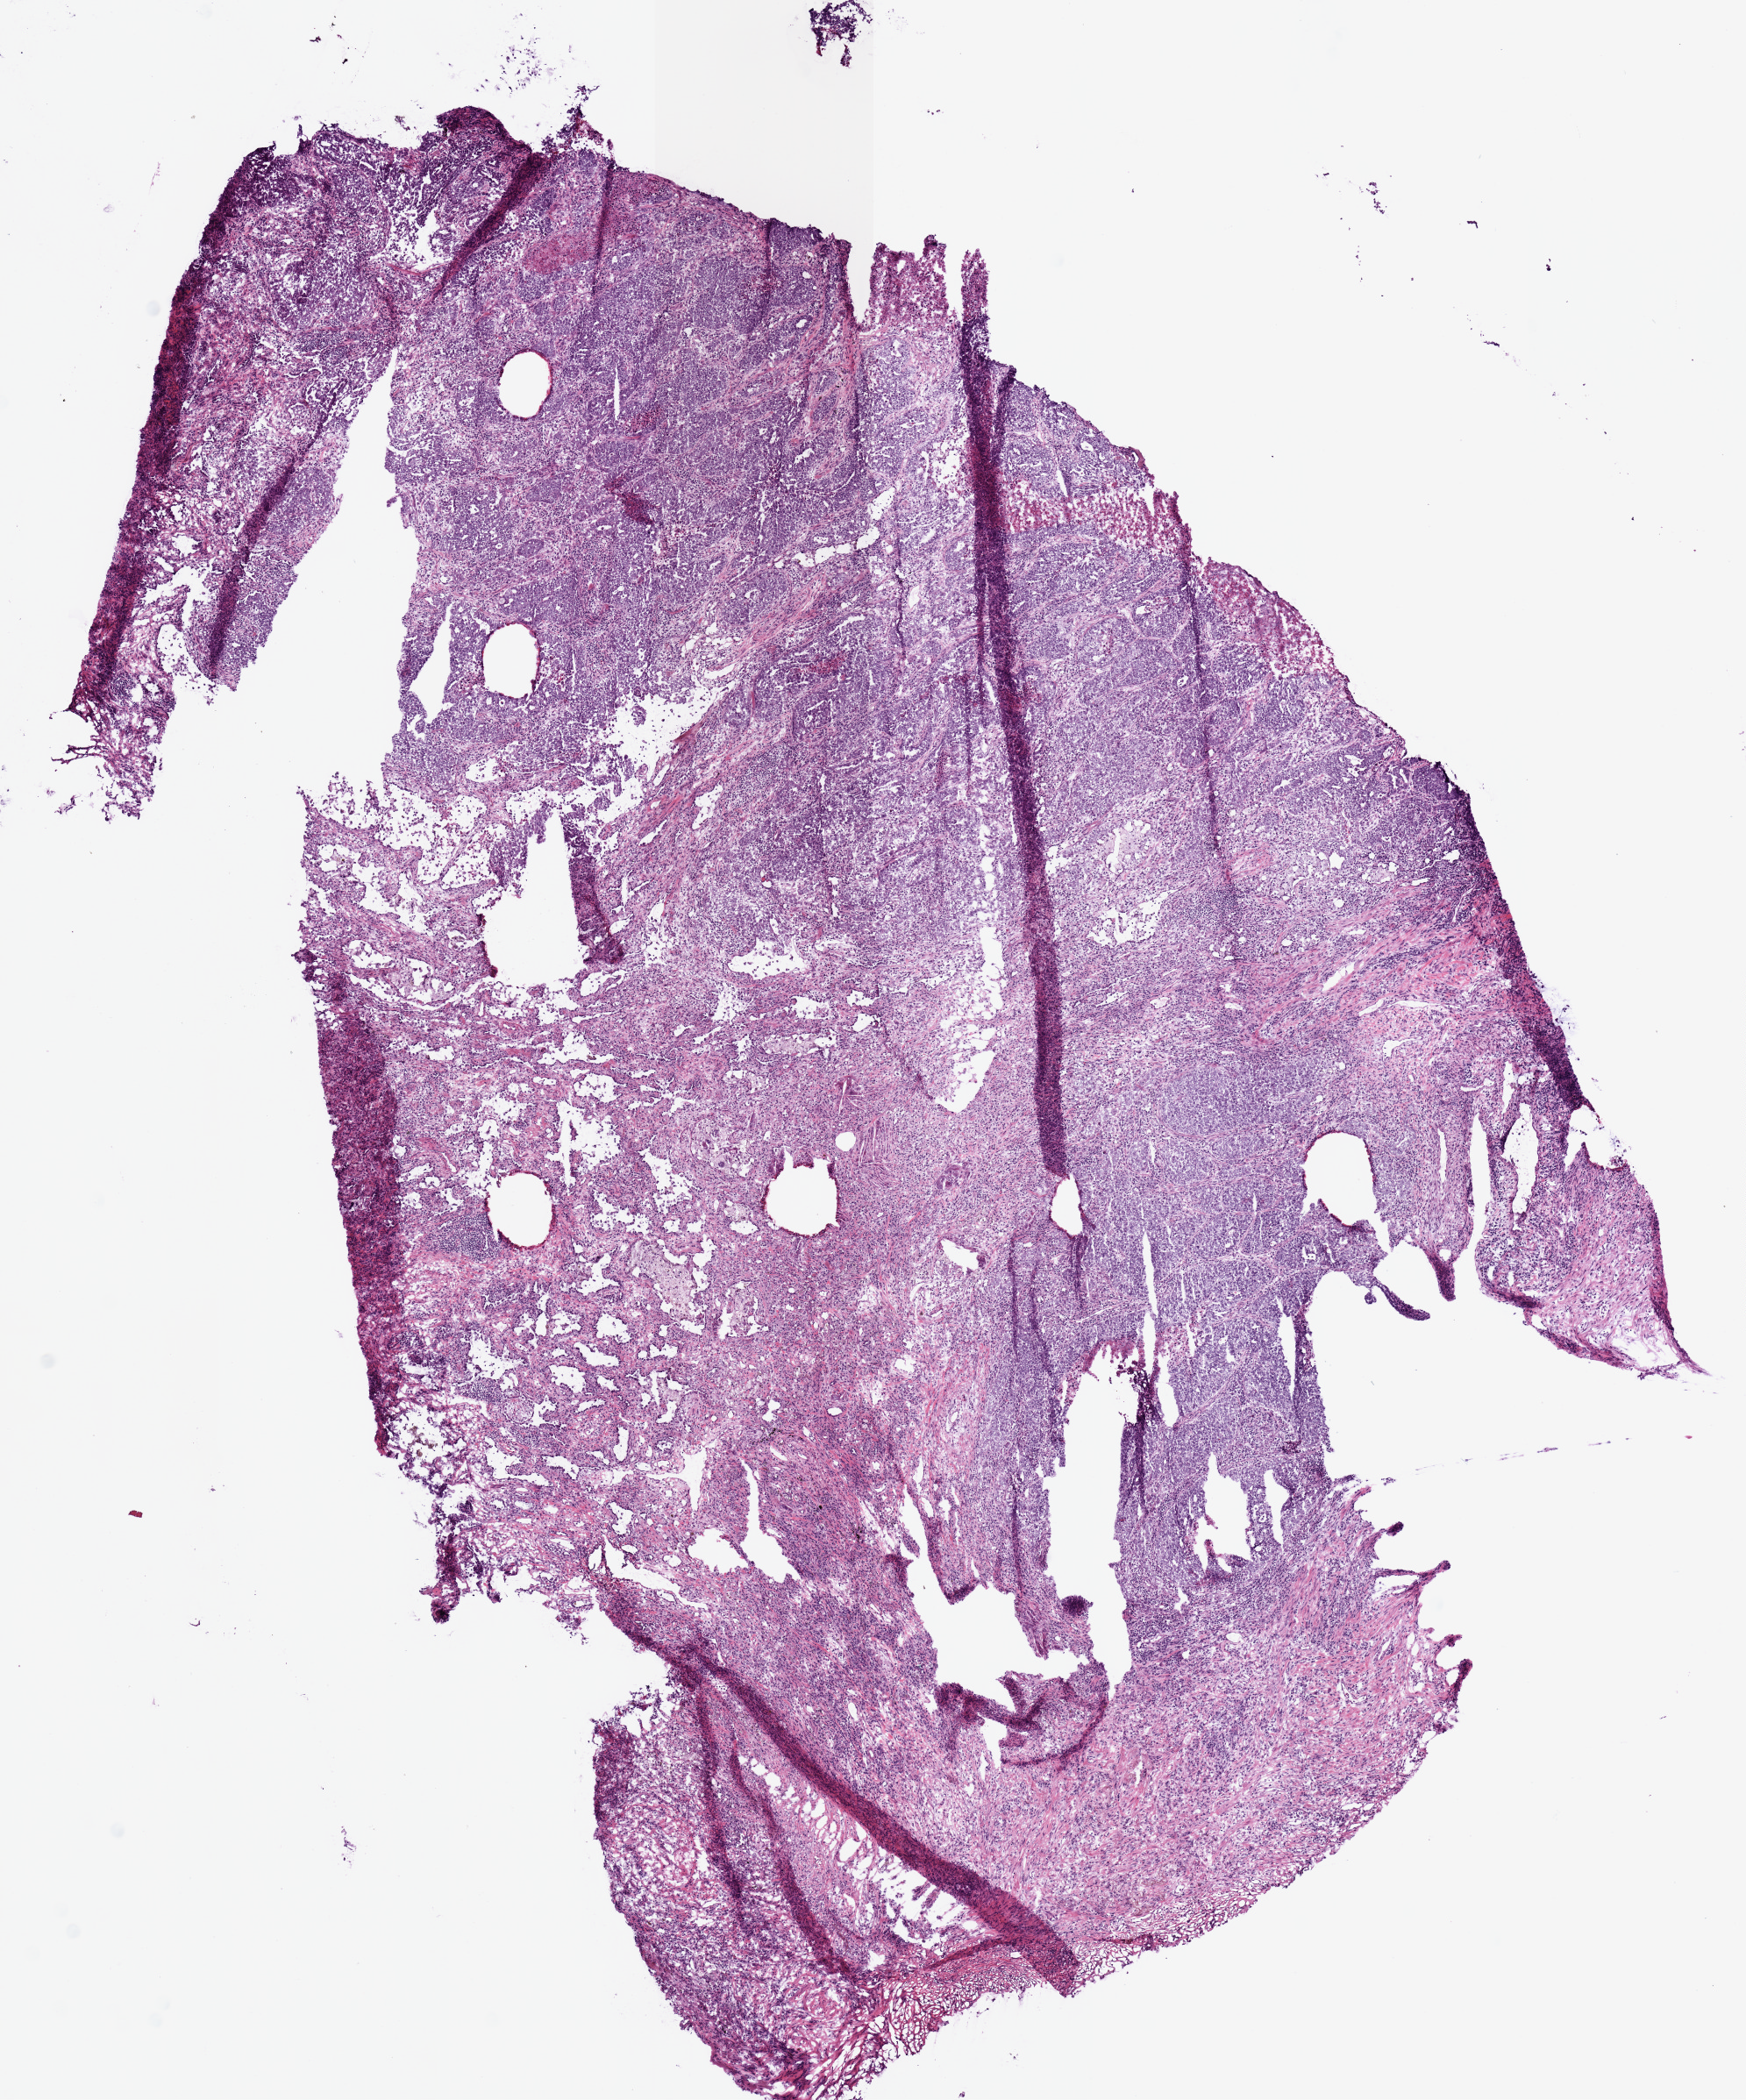
Digitized H&E-stained tissue section (whole slide) — shown as a low-resolution overview of the whole scanned area (about 7.9 x 9.5 mm, acquisition: 20x scan); frozen section; primary tumour sample from the lung. Patient: female, age at initial diagnosis 58 years. Composition of this section per pathologist review: tumour cells 90%, tumour nuclei 80%.
Diagnosis: Adenocarcinoma, NOS (upper lobe, lung).